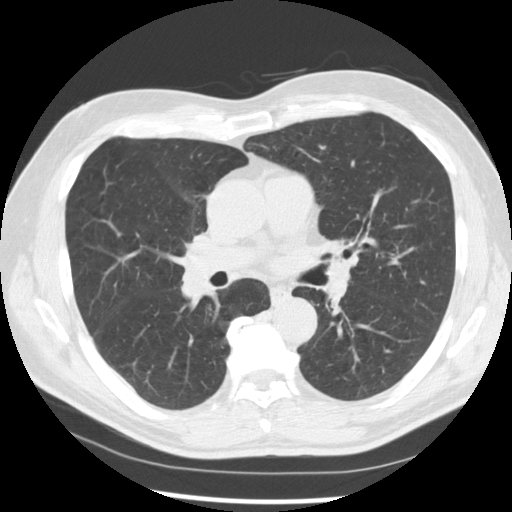
Low-dose screening chest CT, axial slice; baseline annual screen; lung window (W 1500 / L -600 HU); 2.5 mm slice thickness; 120 kVp. Male participant, aged 67 years at enrolment. Current smoker at enrolment.
• Lesion marked by an expert reader, box from (x=161, y=249) to (x=229, y=312) px.
• Reader record for this screening exam (exam-level; its link to the box is not recorded): non-calcified nodule or mass ≥4 mm, left lower lobe, 15 × 15 mm, spiculated (stellate) margins, soft tissue attenuation.
• Note: the box lies in the patient's right hemithorax on this image, whereas the reader's record names the left lung; they may be different findings.
• Official screen result: positive, change unspecified: nodule(s) >= 4 mm or enlarging nodule(s), mass(es), or other non-specific abnormalities suspicious for lung cancer.